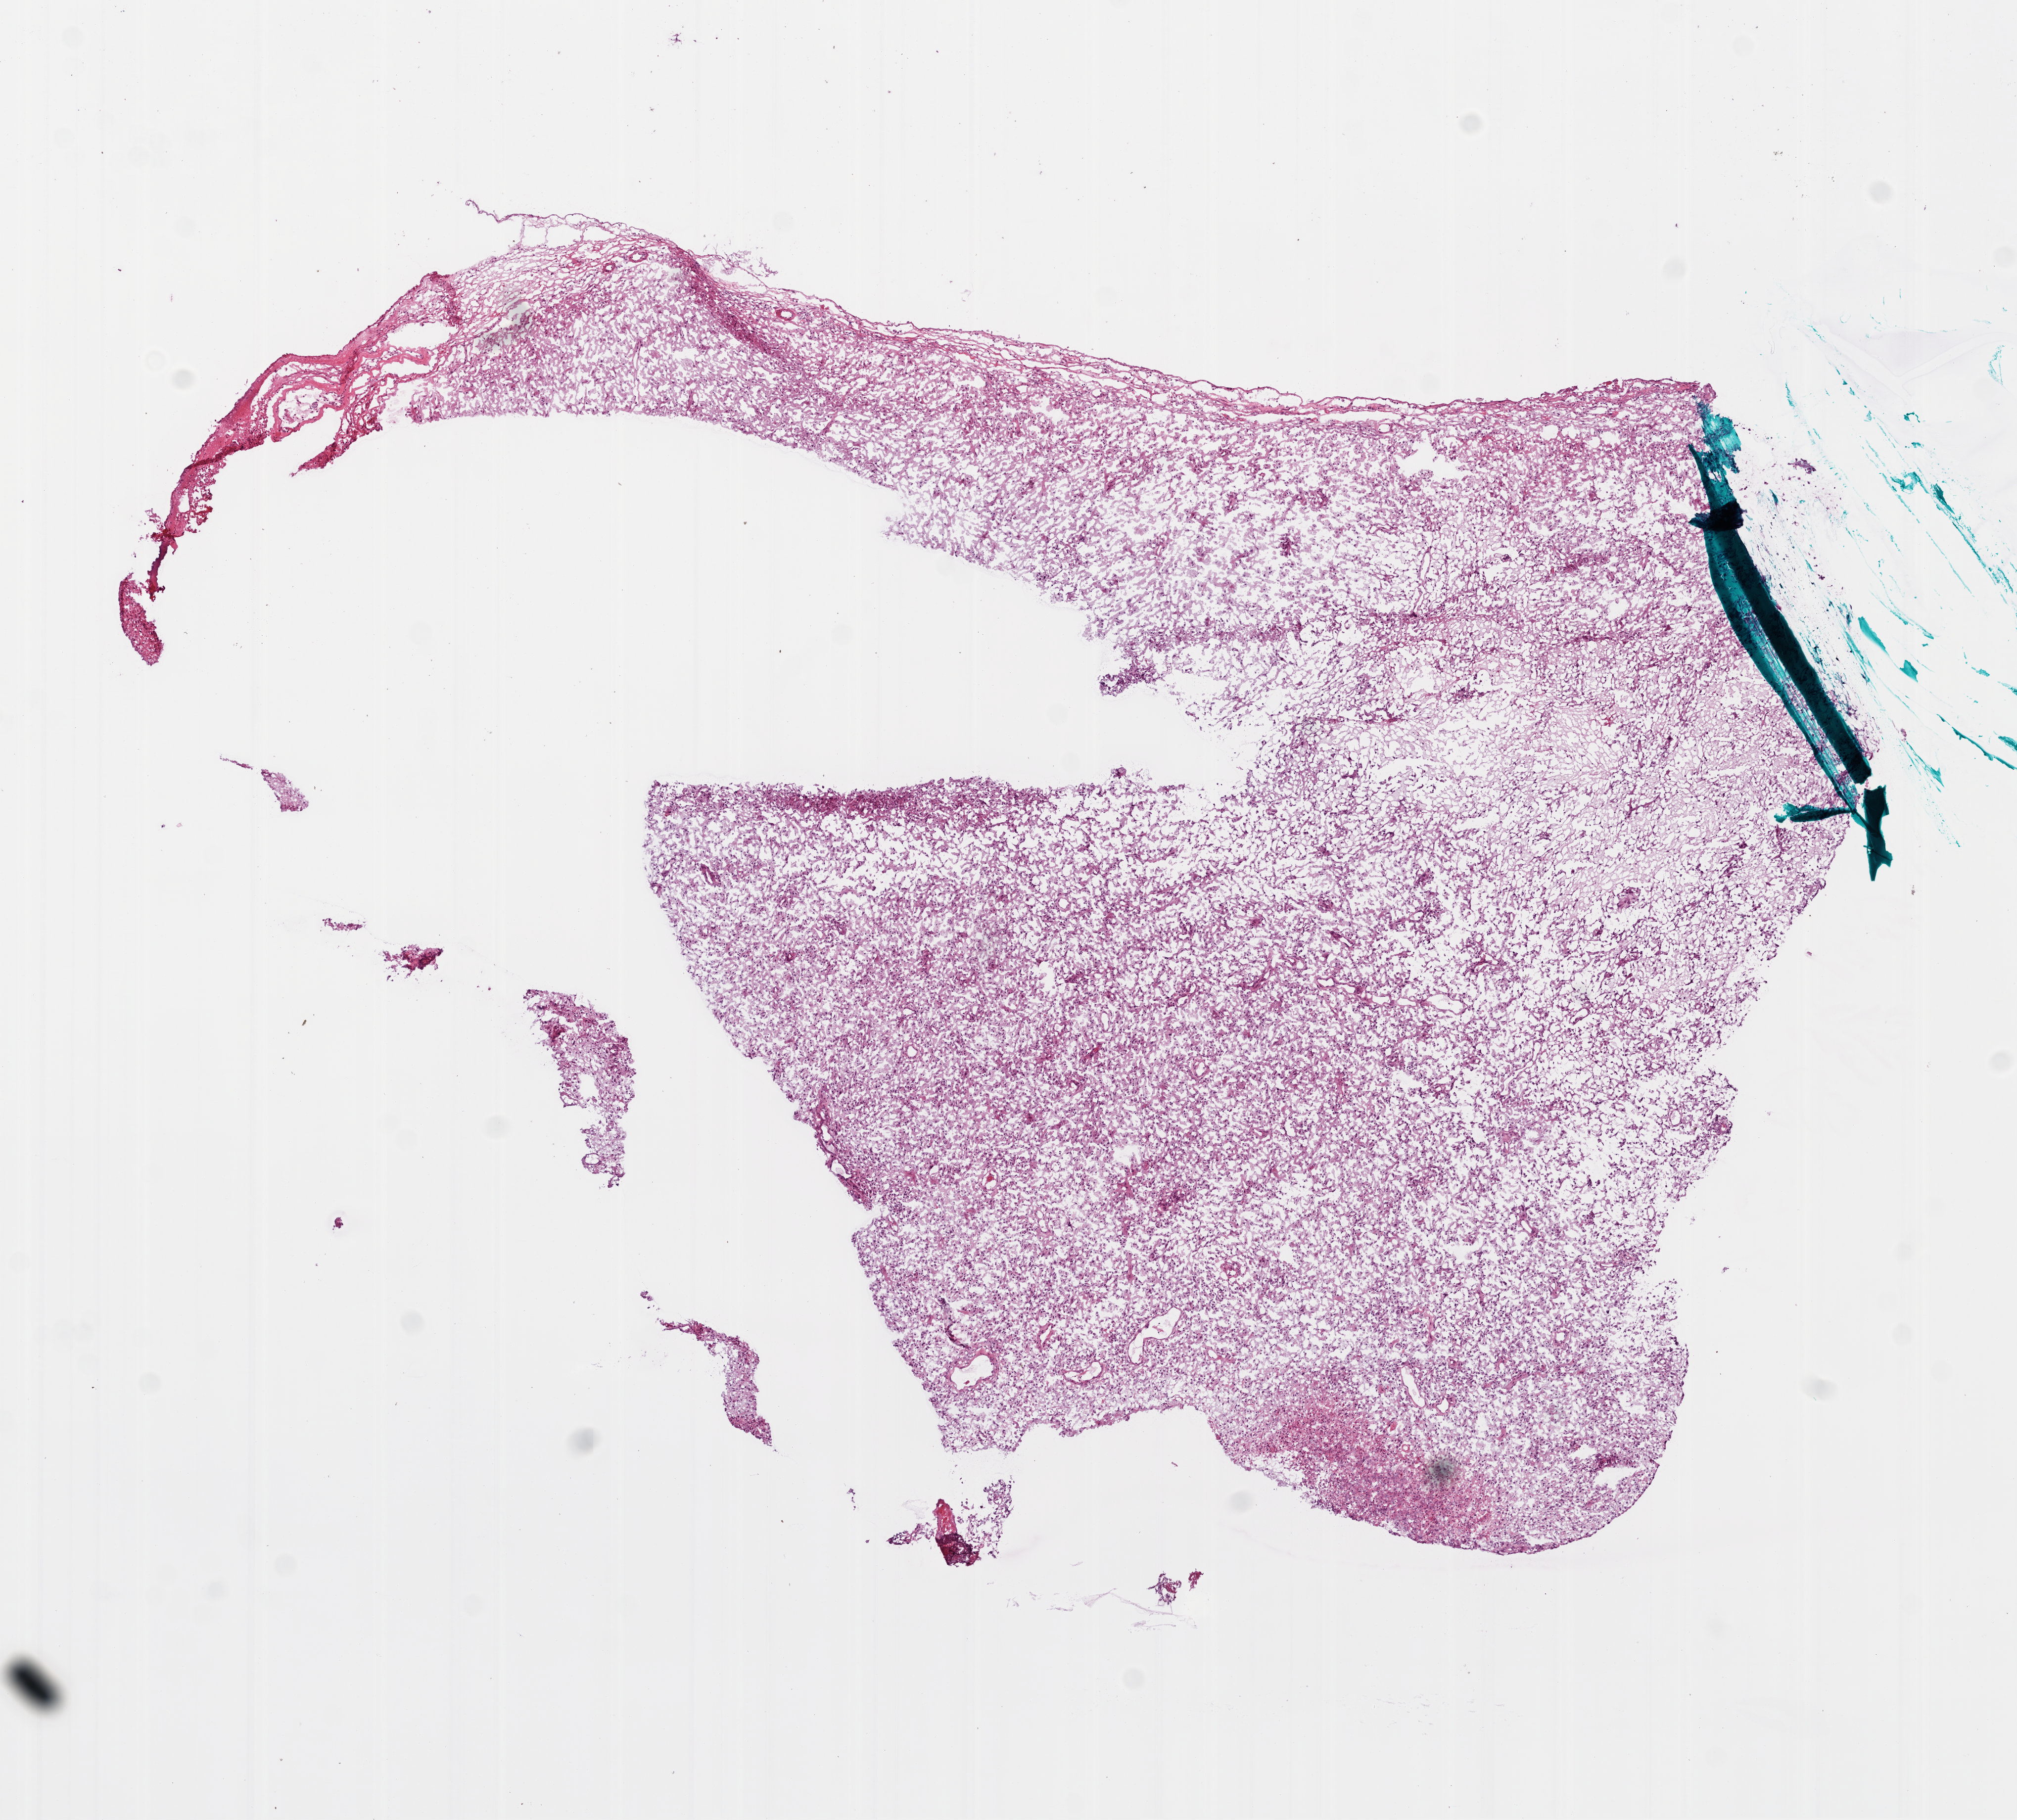
H&E whole-slide image, shown as a low-resolution overview of the whole scanned area (about 8.2 x 7.4 mm, acquisition: 20x scan). Frozen section from the bottom of the tissue portion. Brain, primary tumour sample. Female patient; age at initial diagnosis 75 years. Slide review estimates, as recorded: tumour cells 75%, tumour nuclei 90%, normal cells 0%, stromal cells 0%, necrosis 25%.
Histologic diagnosis: Glioblastoma.